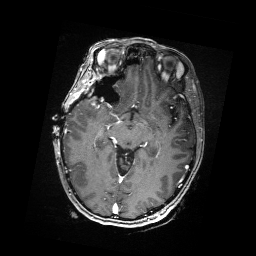
Brain MRI from a brain-tumour surgery series, one axial slice; position 102 of 176 along the scan axis; T1-weighted post-contrast; 1 mm slice thickness; 256 × 256 image matrix, field of view 256 × 256 mm. Case-level facts recorded for this patient, not image findings: histopathology: Metastatic Carcinoma from Breast primary; tumour location: Right Frontal.
Structures marked on this image (manually delineated by an expert):
- residual tumour: bounding box (x1, y1, x2, y2) in pixels: (92, 92, 95, 95)